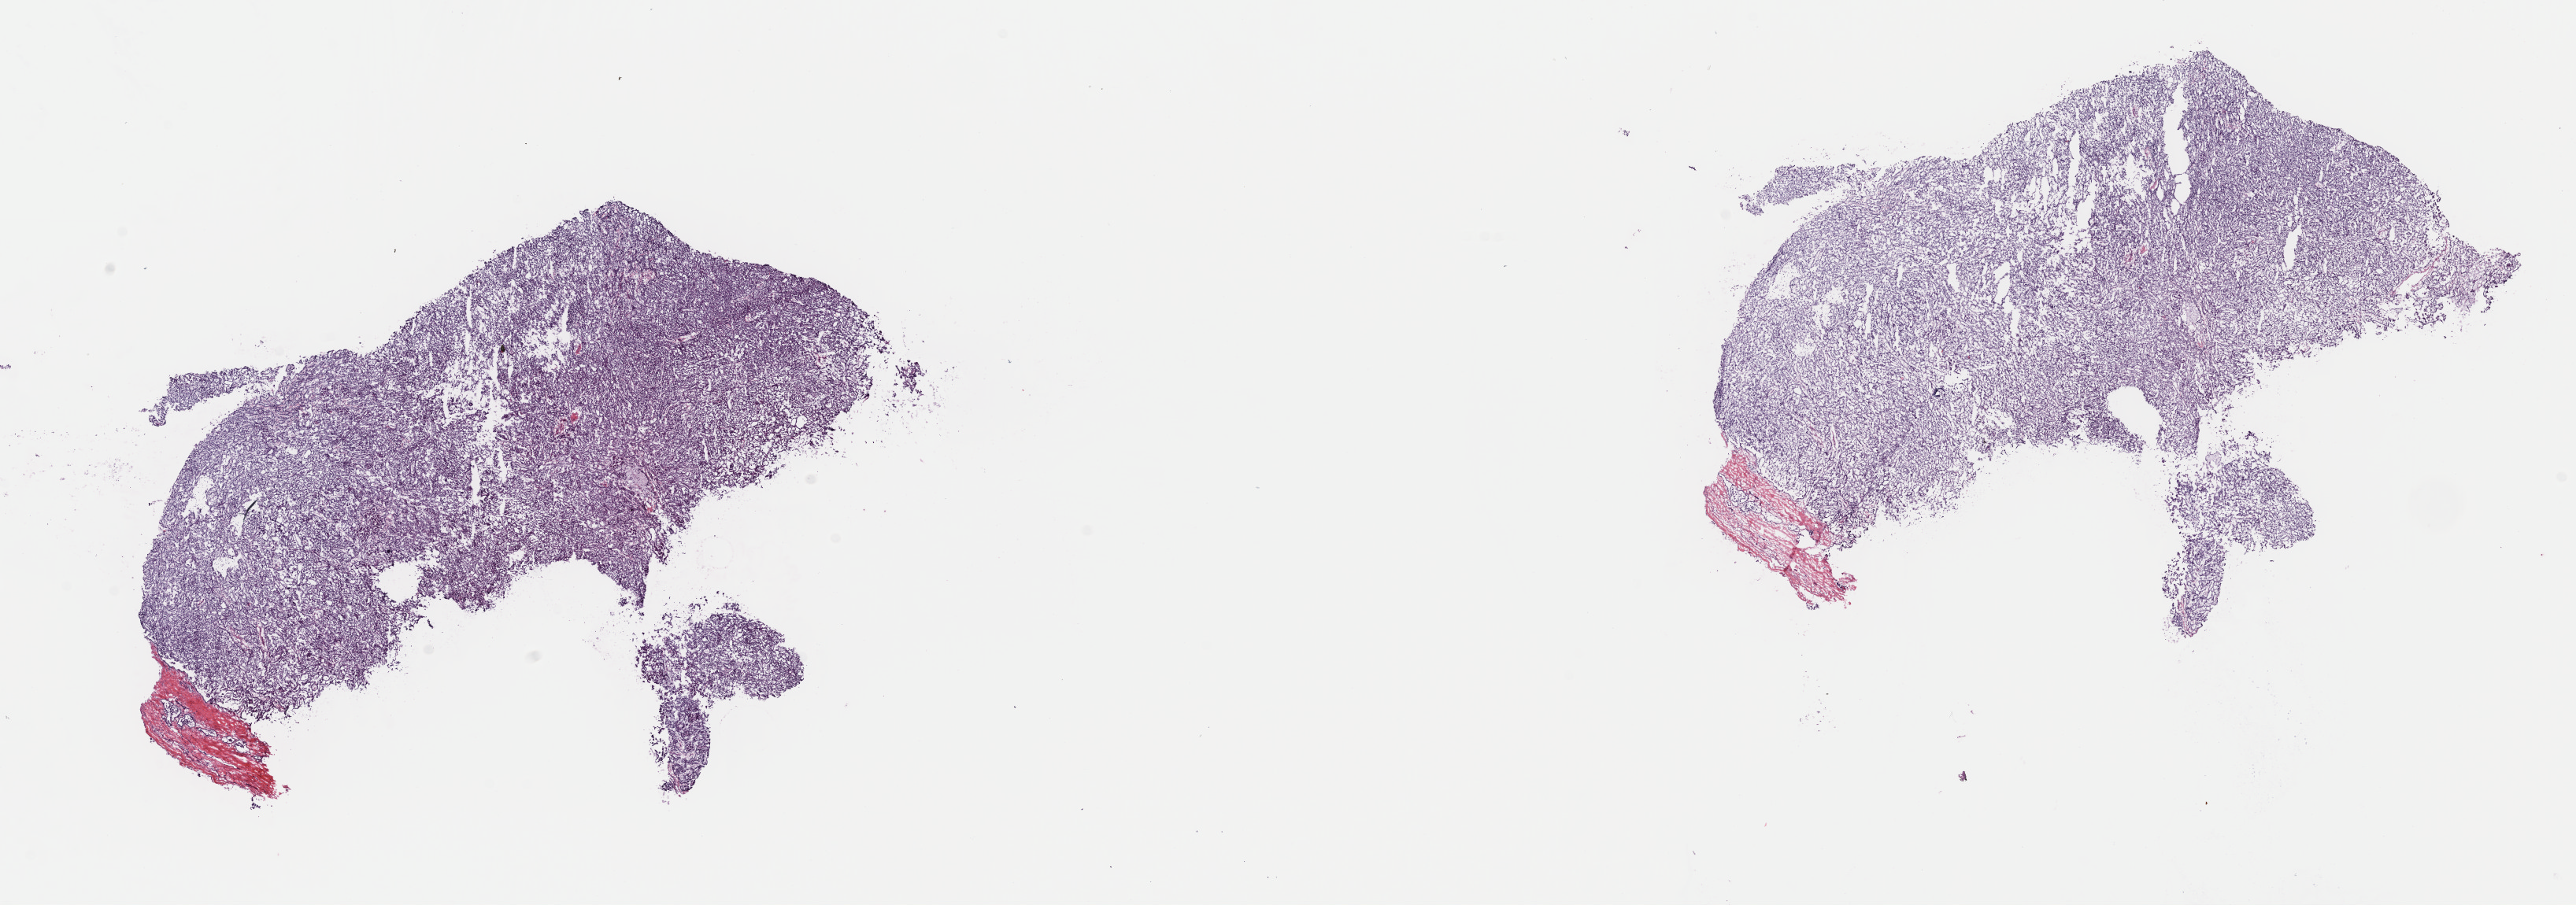
H&E whole-slide image, a low-resolution overview of the entire scanned area, about 25.8 x 9.1 mm. Frozen section from the top of the tissue portion. Primary tumour sample from the kidney. Male, age 44 years at initial diagnosis. Pathologist review of this section (percent, as recorded): tumour cells 100%, tumour nuclei 80%, normal cells 0%, stromal cells 0%, necrosis 0%. Infiltration values recorded for this section: lymphocyte infiltration 1%, monocyte infiltration 2%, neutrophil infiltration 0%.
• AJCC pathologic stage: I (7th edition)
• pathologic diagnosis: Papillary adenocarcinoma, NOS
• laterality: left